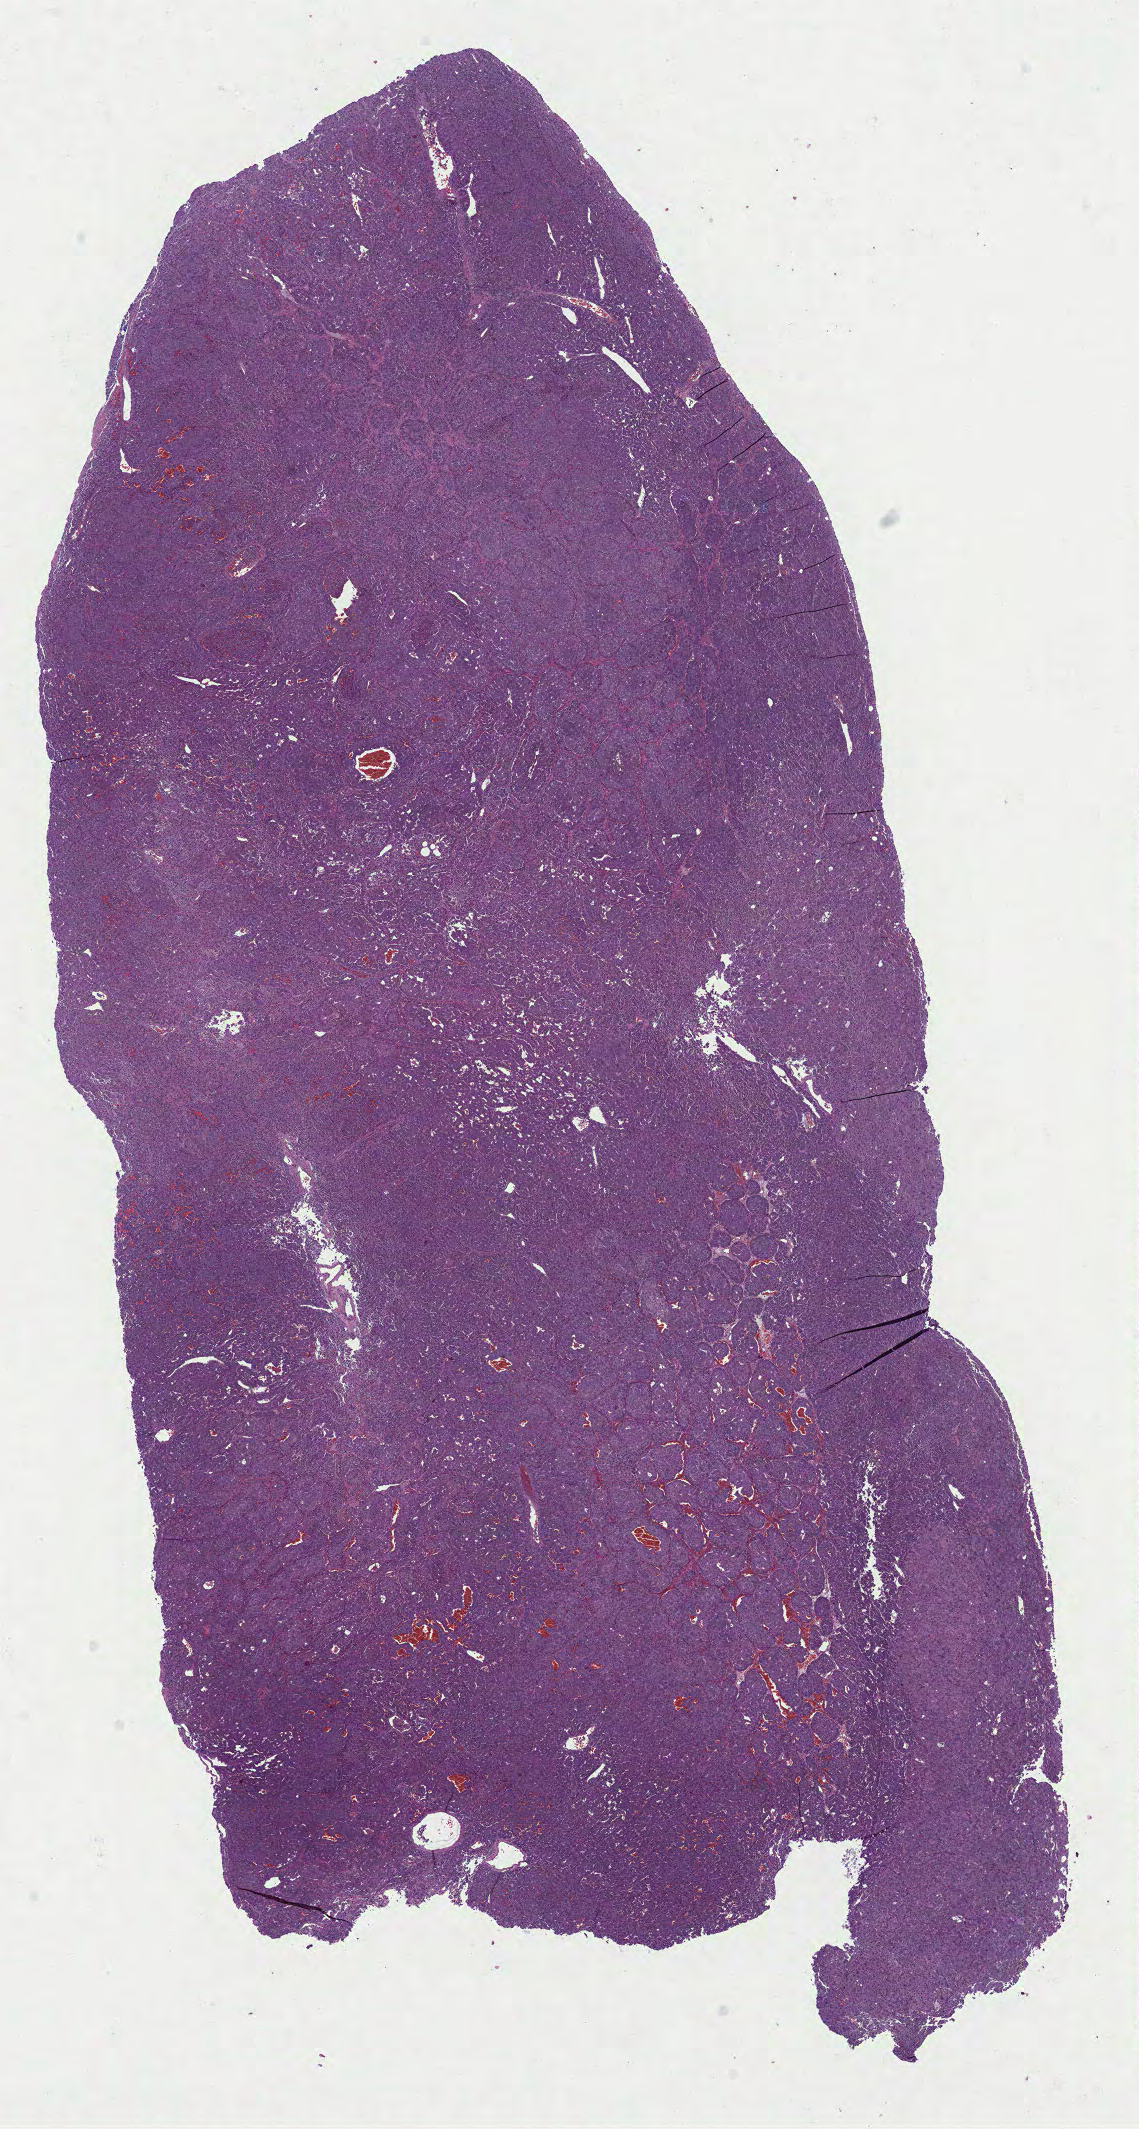
Whole-slide histology image, H&E-stained — shown as a low-resolution overview of the whole scanned area (about 9.2 x 17.2 mm, slide scanned at 40x); formalin-fixed paraffin-embedded (FFPE) diagnostic section; primary tumour sample from the adrenal gland. Patient: male, age at initial diagnosis 39 years.
Laterality: right. Pathologic diagnosis: Pheochromocytoma, malignant.